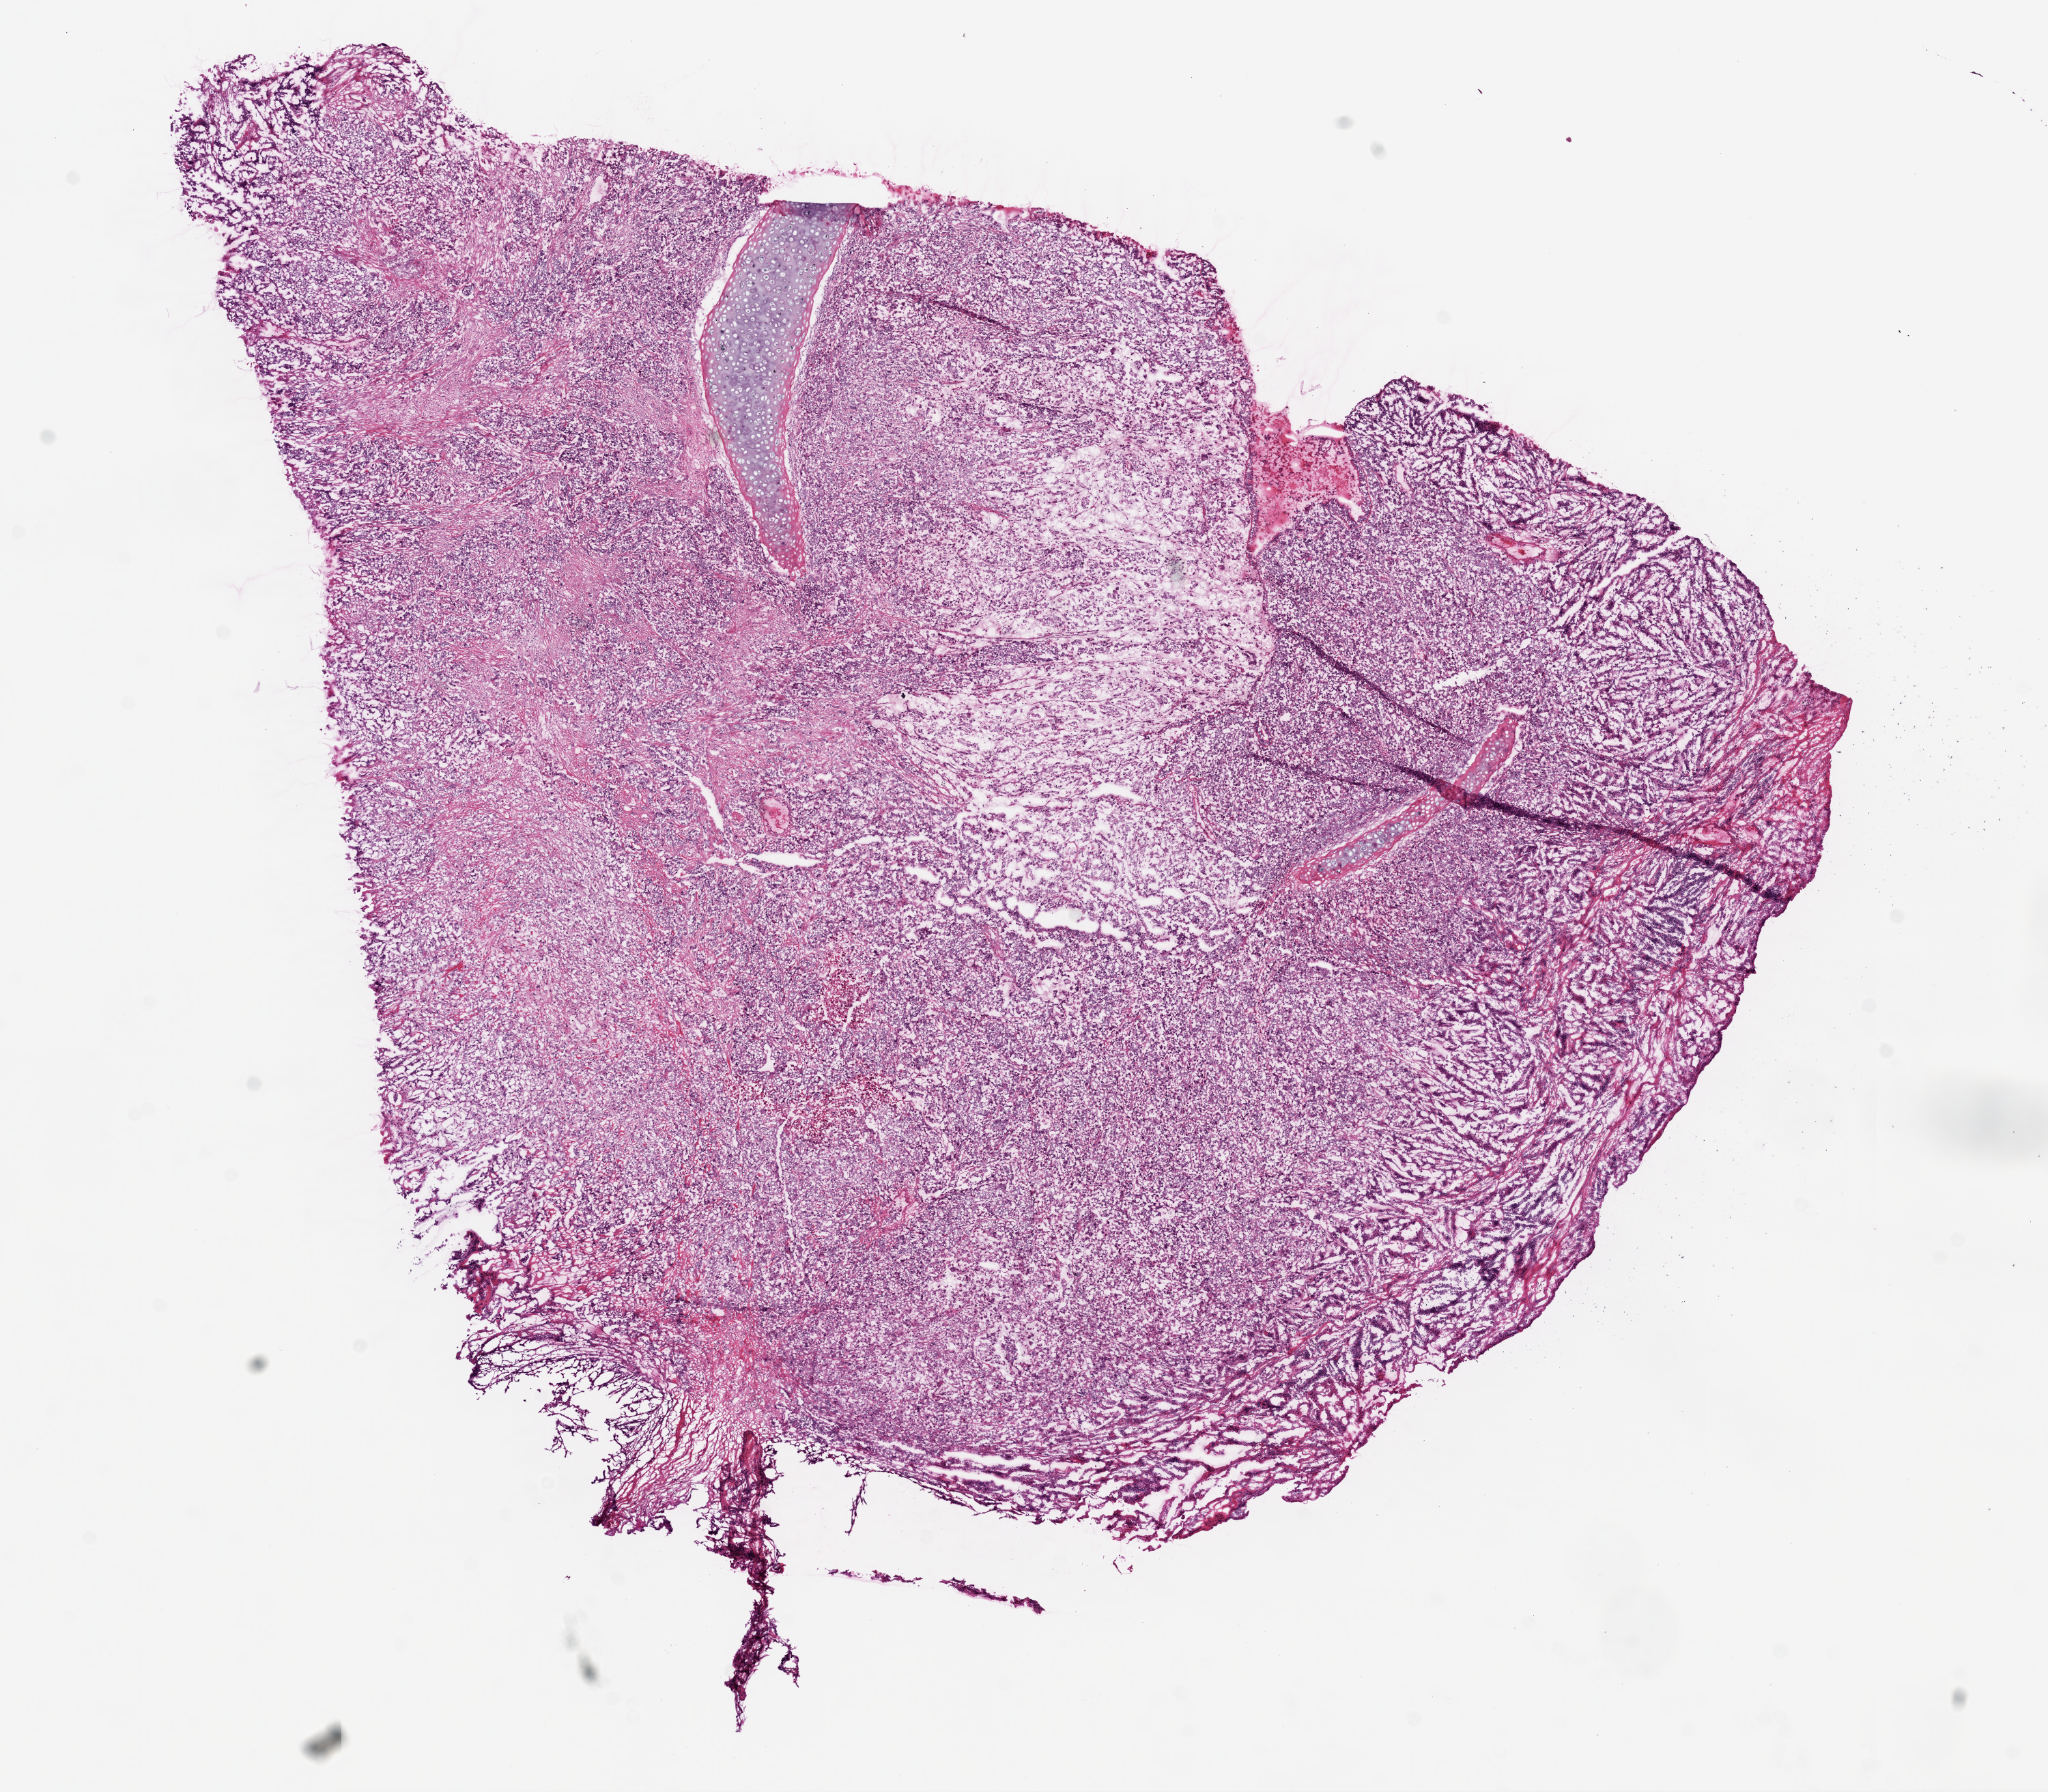
Whole-slide histology image, H&E-stained, a low-resolution overview of the entire scanned area, about 12.0 x 10.5 mm (from a 20x scan), frozen section from the top of the tissue portion, sample: primary tumour, lung. Male, age 65 years at initial diagnosis. Pathologist review of this section (percent, as recorded): tumour cells 85%, tumour nuclei 80%, normal cells 0%, stromal cells 10%, necrosis 5%. Infiltration values recorded for this section: lymphocyte infiltration 5%, monocyte infiltration 2%, neutrophil infiltration 5%.
Histologic diagnosis: Squamous cell carcinoma, NOS. TNM: T2 N2 M0. AJCC pathologic stage: IIIA.